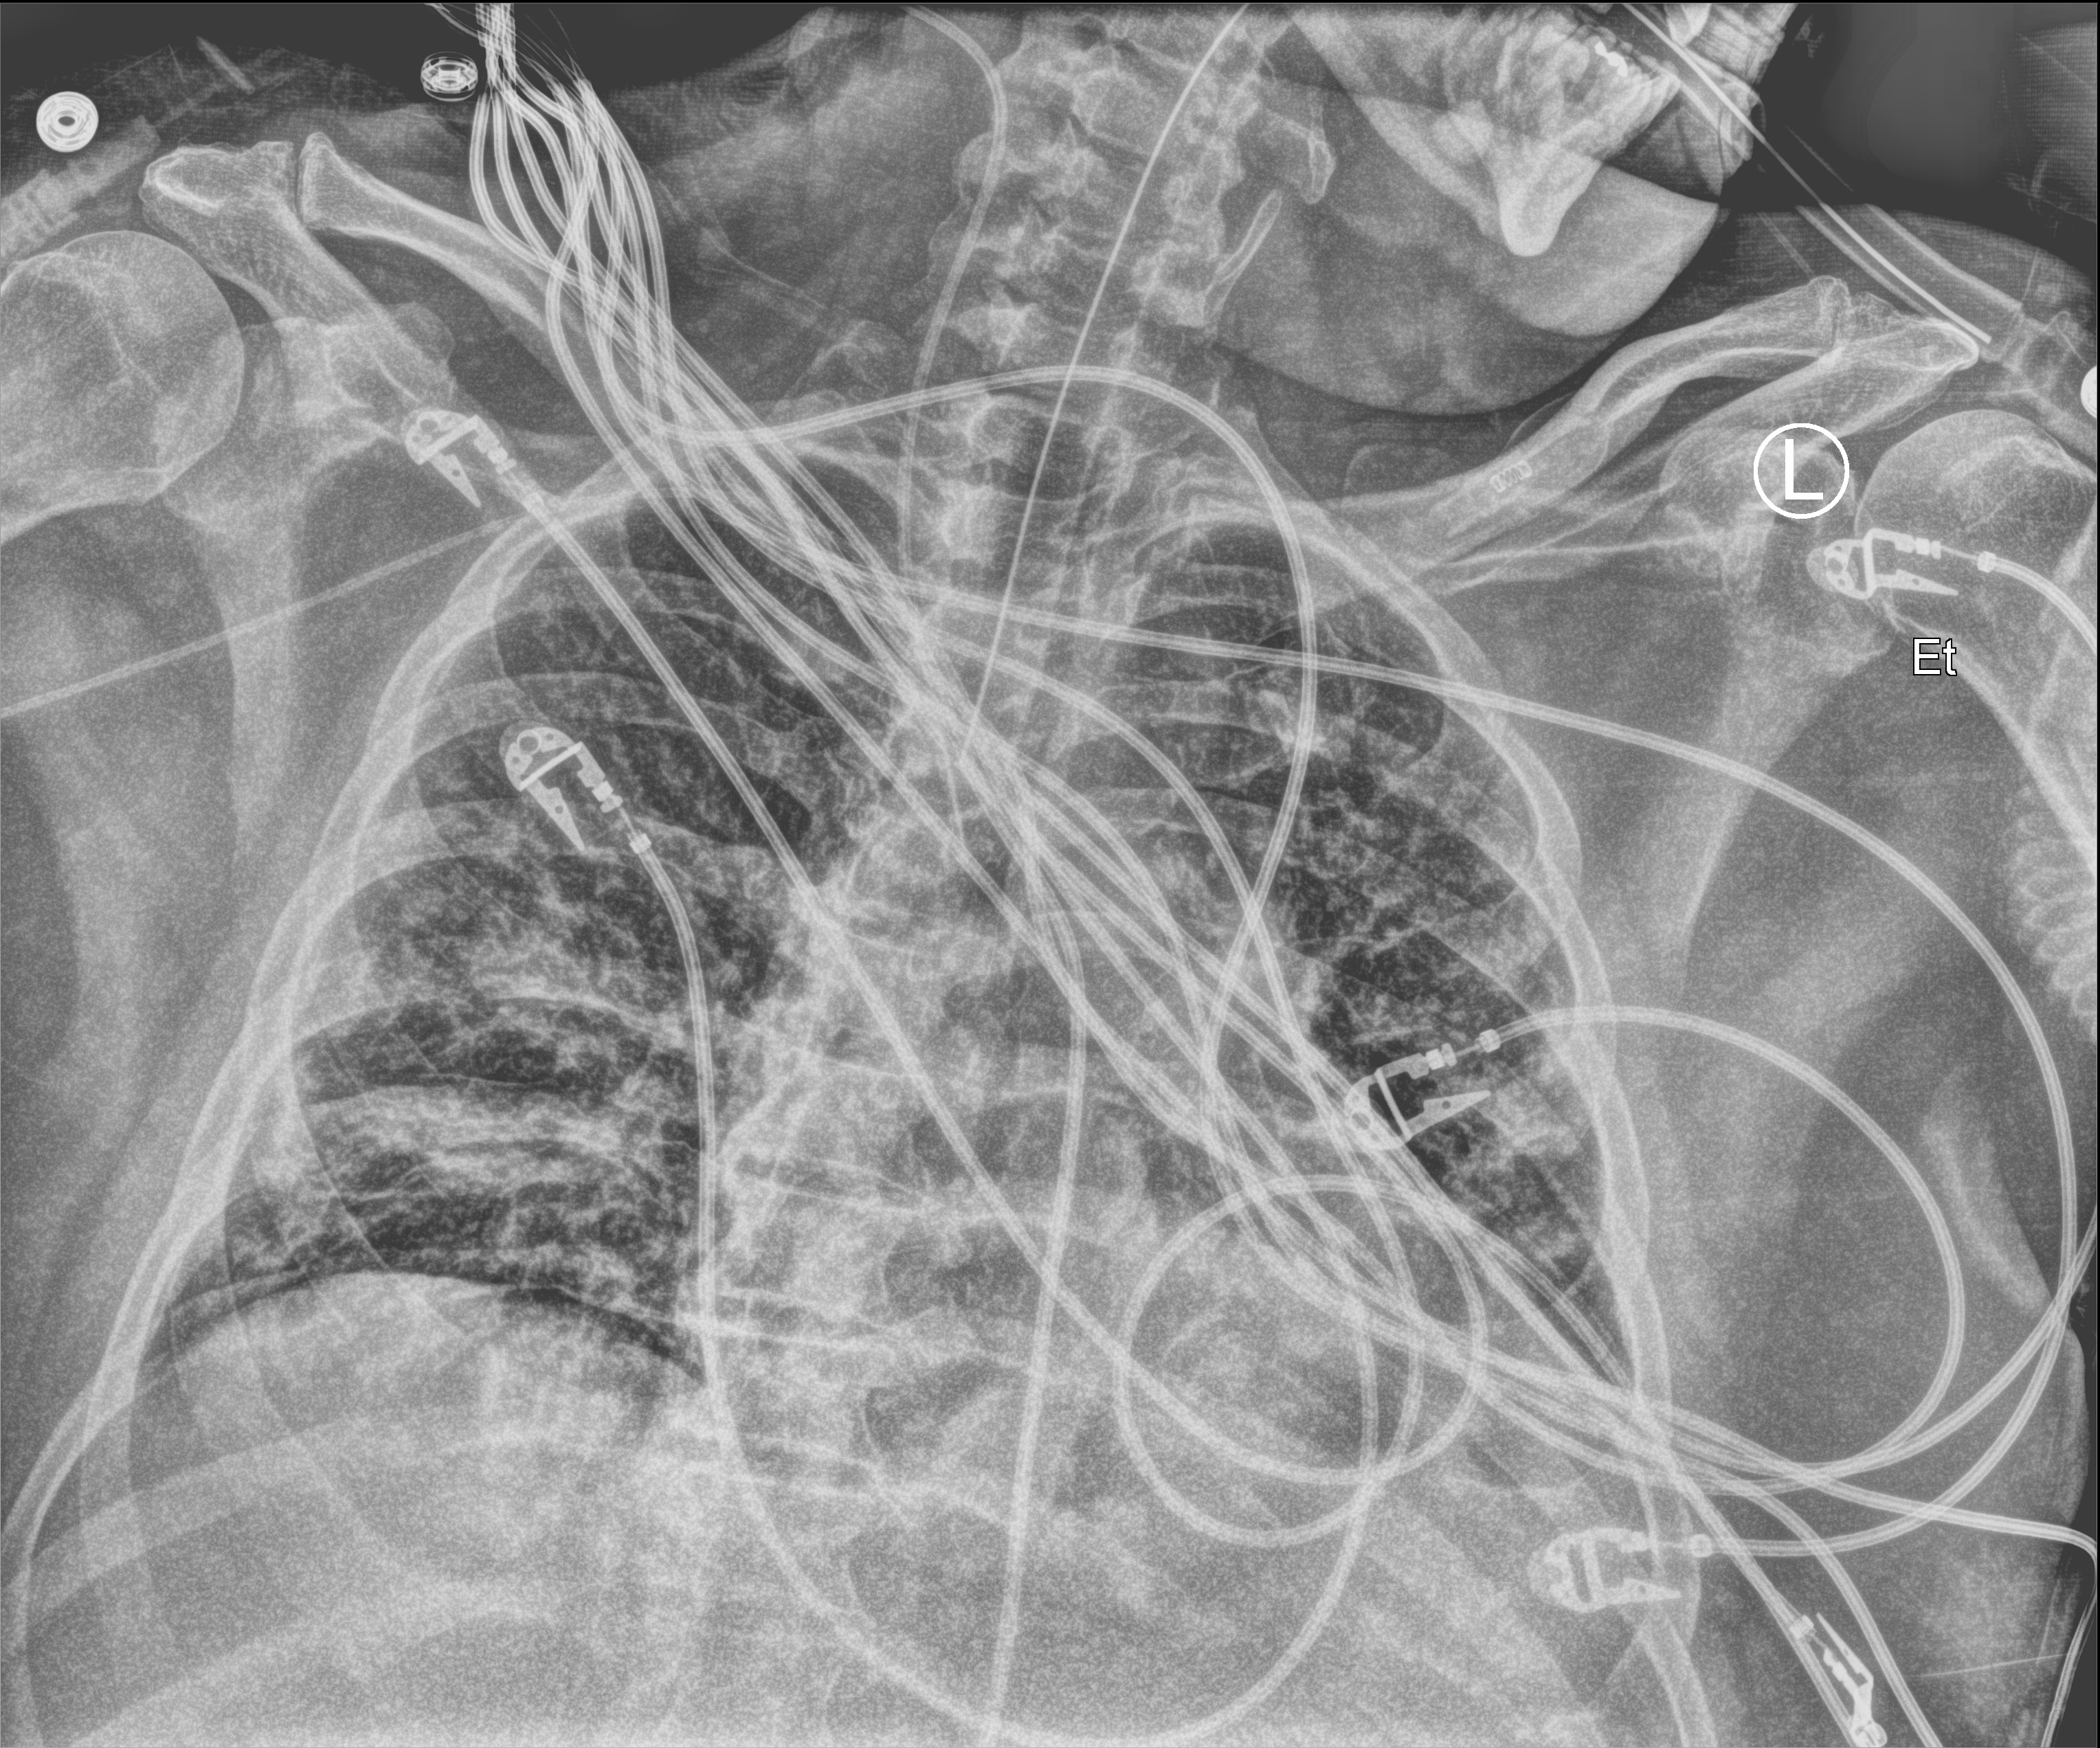
Portable chest radiograph, anteroposterior (AP) projection. Male patient hospitalised with COVID-19, age 18–59 years.
Admission-level facts for this patient (not findings on this image; timing relative to this image not recorded): mechanically ventilated during this hospital stay: yes; admitted to intensive care during this hospital stay: yes; length of hospital stay: 21 days.